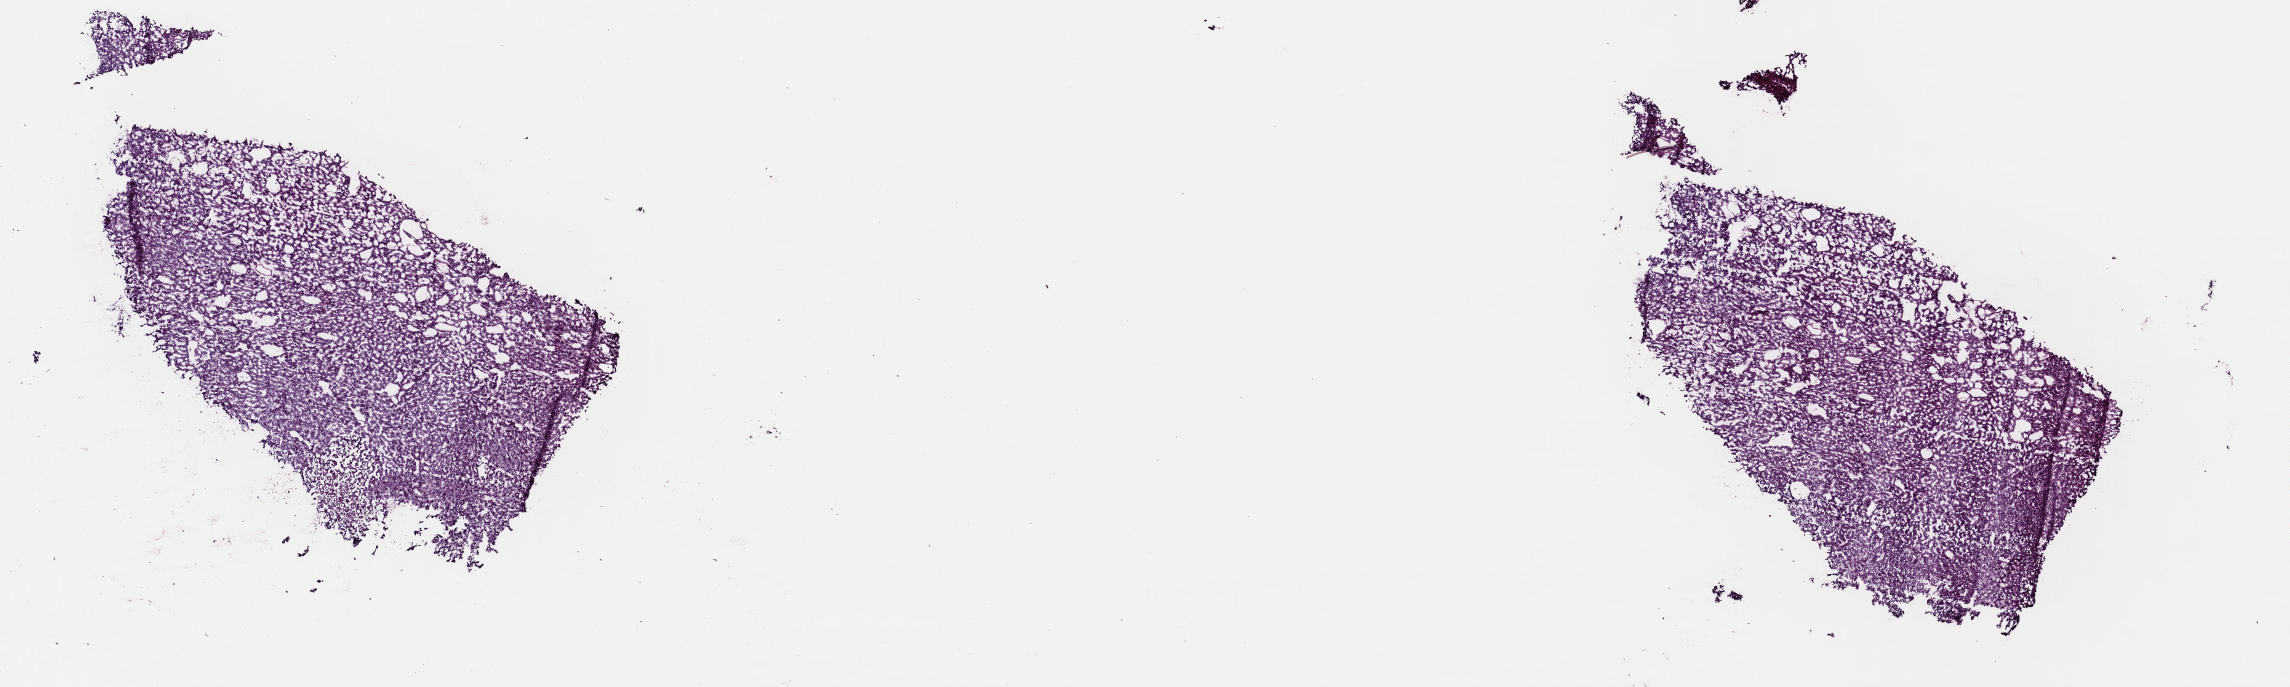
H&E-stained whole-slide image, shown as a low-resolution overview of the whole scanned area (about 18.1 x 5.4 mm, from a 40x scan), frozen section from the top of the tissue portion, primary tumour sample from the liver. Patient: male, age at initial diagnosis 80 years.
Diagnosis: Hepatocellular carcinoma, NOS.